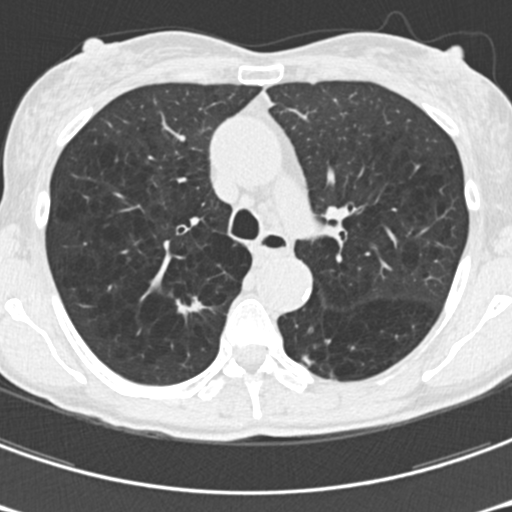
Axial slice from a low-dose chest CT screening exam. Third screening round (two years after baseline). Lung window (W 1500 / L -600 HU). Standard (soft-tissue) reconstruction kernel (B30f). Slice 59 of 176 in the series. 512 × 512 image matrix. Female participant, aged 61 years at enrolment. Current smoker at enrolment.
Lesion marked by an expert reader, bounding box [x1, y1, x2, y2] px = [162, 284, 217, 337]. The screening reader recorded 2 non-calcified nodules or masses ≥4 mm on this exam (right upper lobe, right upper lobe); which of them this box marks is not recorded. Lung cancer was diagnosed 77 days after this screen: non-small cell carcinoma, right upper lobe, undifferentiated (G4), stage IA (AJCC 6th edition), 15 mm at pathology.